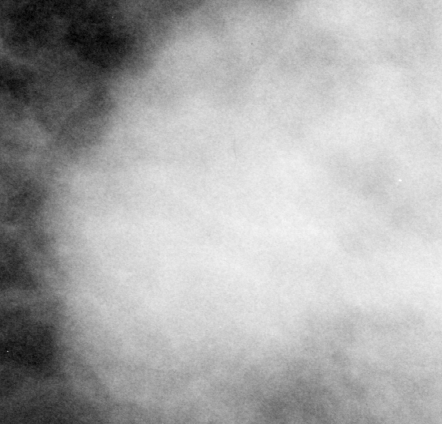
Cropped region of a digitized screen-film mammogram centred on a radiologist-marked abnormality; left breast; CC view; BI-RADS breast density category 3 (scale 1–4).
Finding: mass, shape lobulated / irregular, margins obscured / ill defined; BI-RADS assessment category 4; subtlety rating 4 on a 1 (subtle) to 5 (obvious) scale; pathology result (as recorded, not read from the image): malignant.